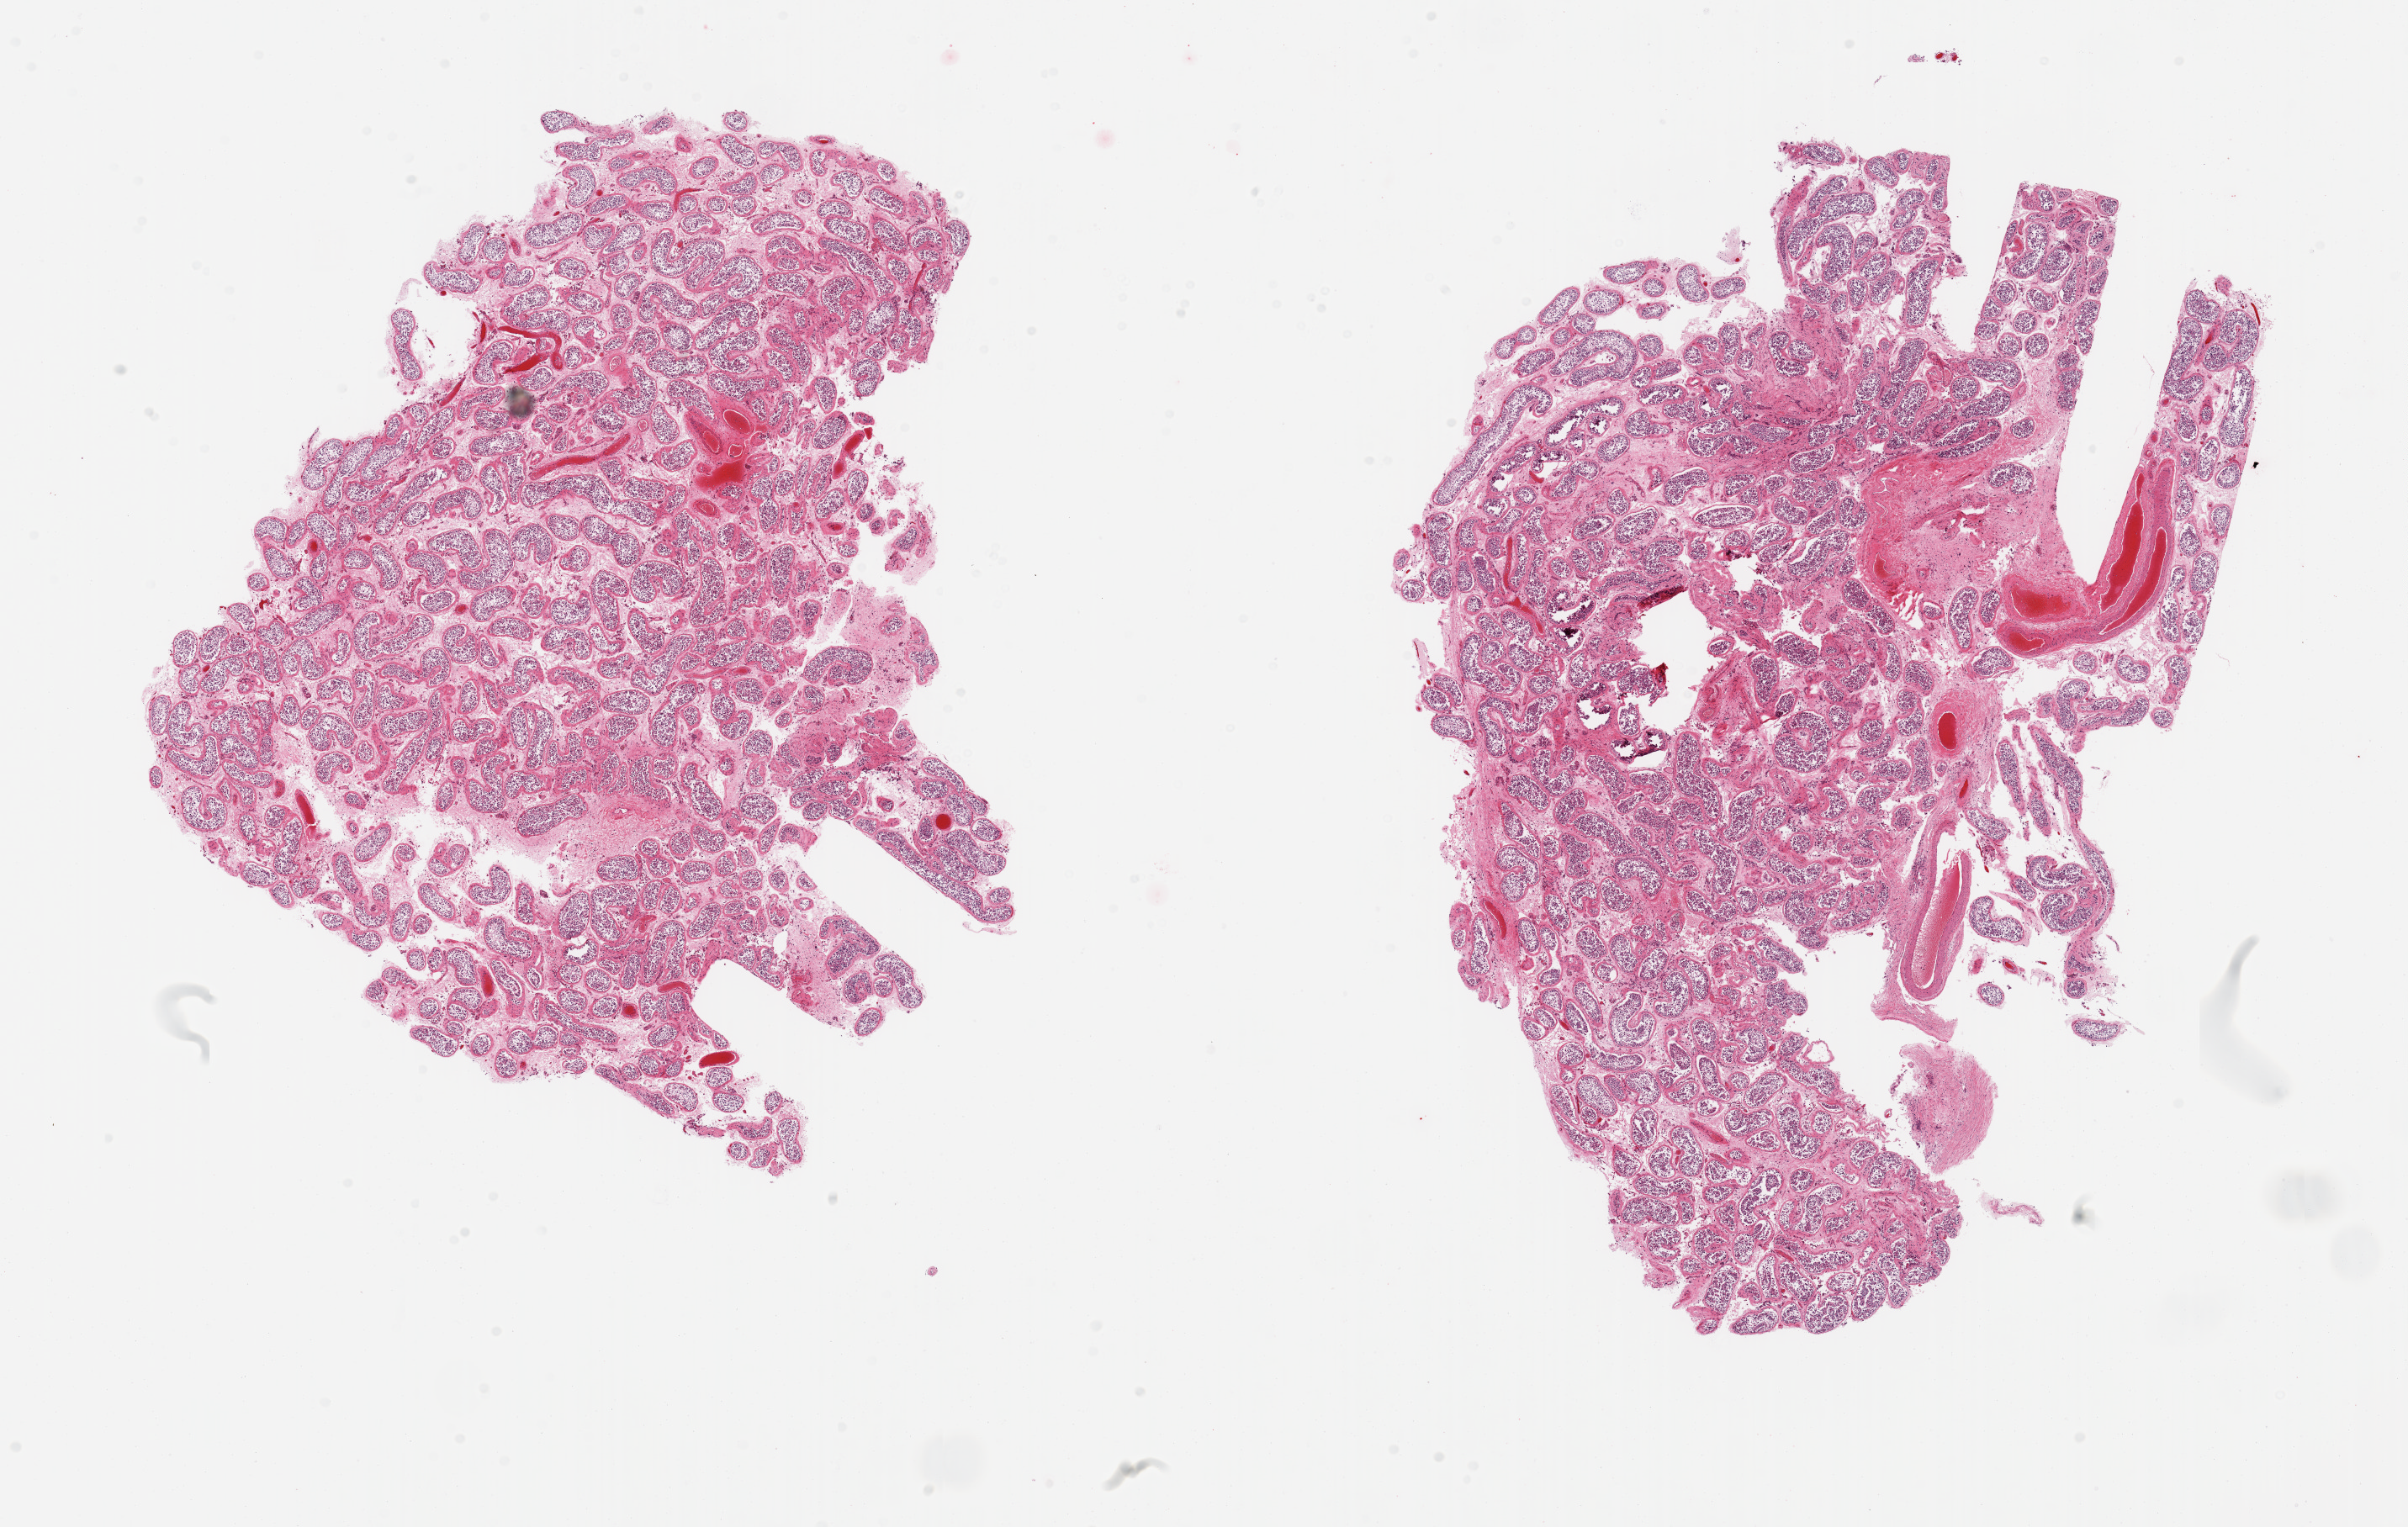
H&E whole-slide image, brightfield — shown as a low-resolution overview of the whole scanned area (about 22.6 x 14.4 mm). PAXgene-fixed paraffin-embedded (PFPE) section. Target tissue: testis. Donor tissue sample. Donor: male.
• reviewer comment on this tissue sample: 2 pieces, moderately advanced autolysis